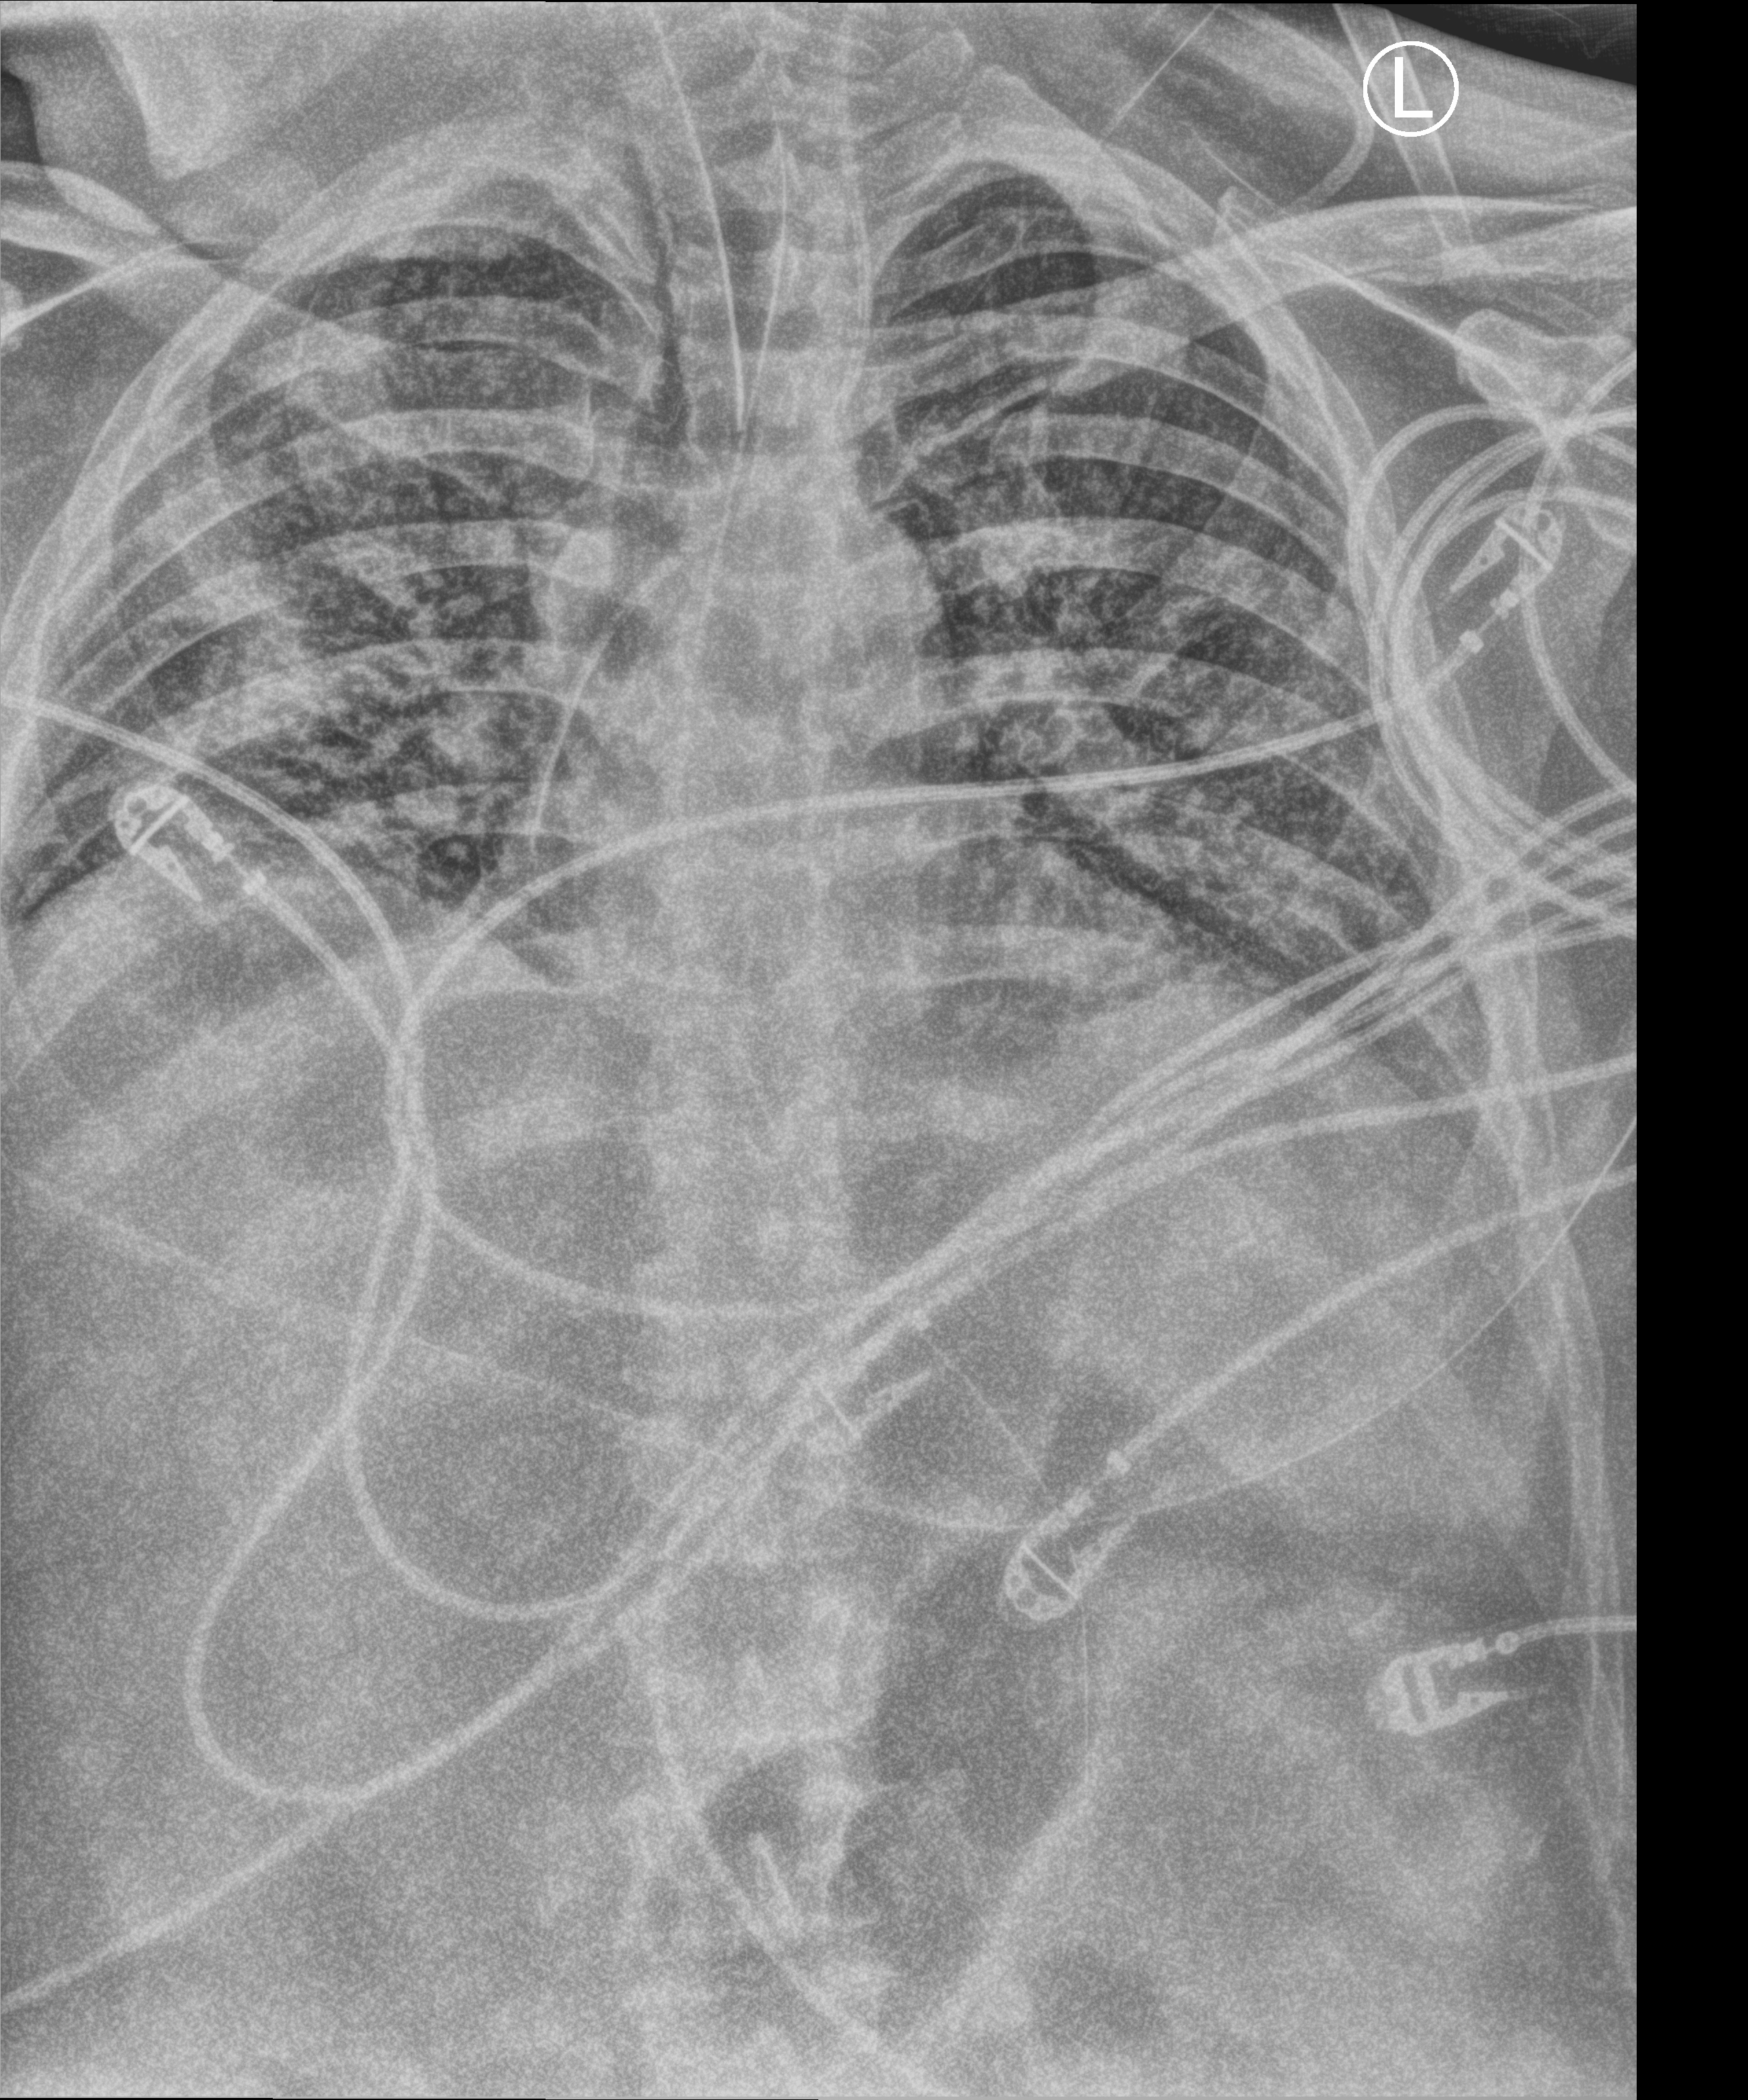
Chest X-ray (portable), anteroposterior (AP) projection. Patient hospitalised with COVID-19; male, aged 18–59 years.
Hospital-stay facts (about this admission, not read from this image; timing relative to this image not recorded):
- mechanically ventilated during this hospital stay: yes
- admitted to intensive care during this hospital stay: yes